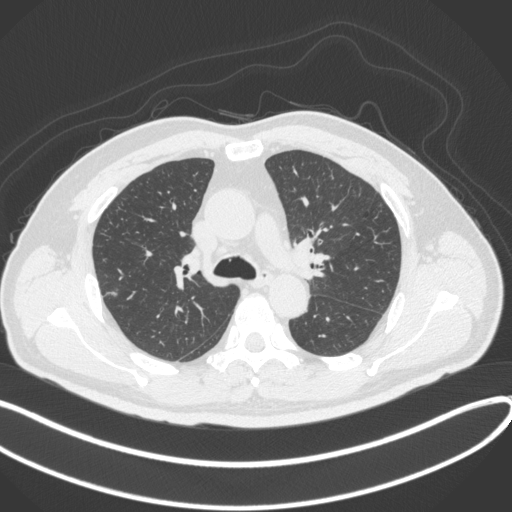
Chest CT, one axial slice. Slice 228 of 373 in the series (ordered by position). 120 kVp. Lung window (W 1500 / L -600 HU). 1 mm slice thickness. 512 × 512 image matrix, field of view 400 × 400 mm. Male patient, age 60 years. From the clinical record (not read from this slice): clinical TNM (as recorded): T1c N0 M0.
Outlined on this slice (bounding box drawn by a radiologist):
- lung tumour (recorded histology: adenocarcinoma): box from (x=103, y=285) to (x=123, y=301) px